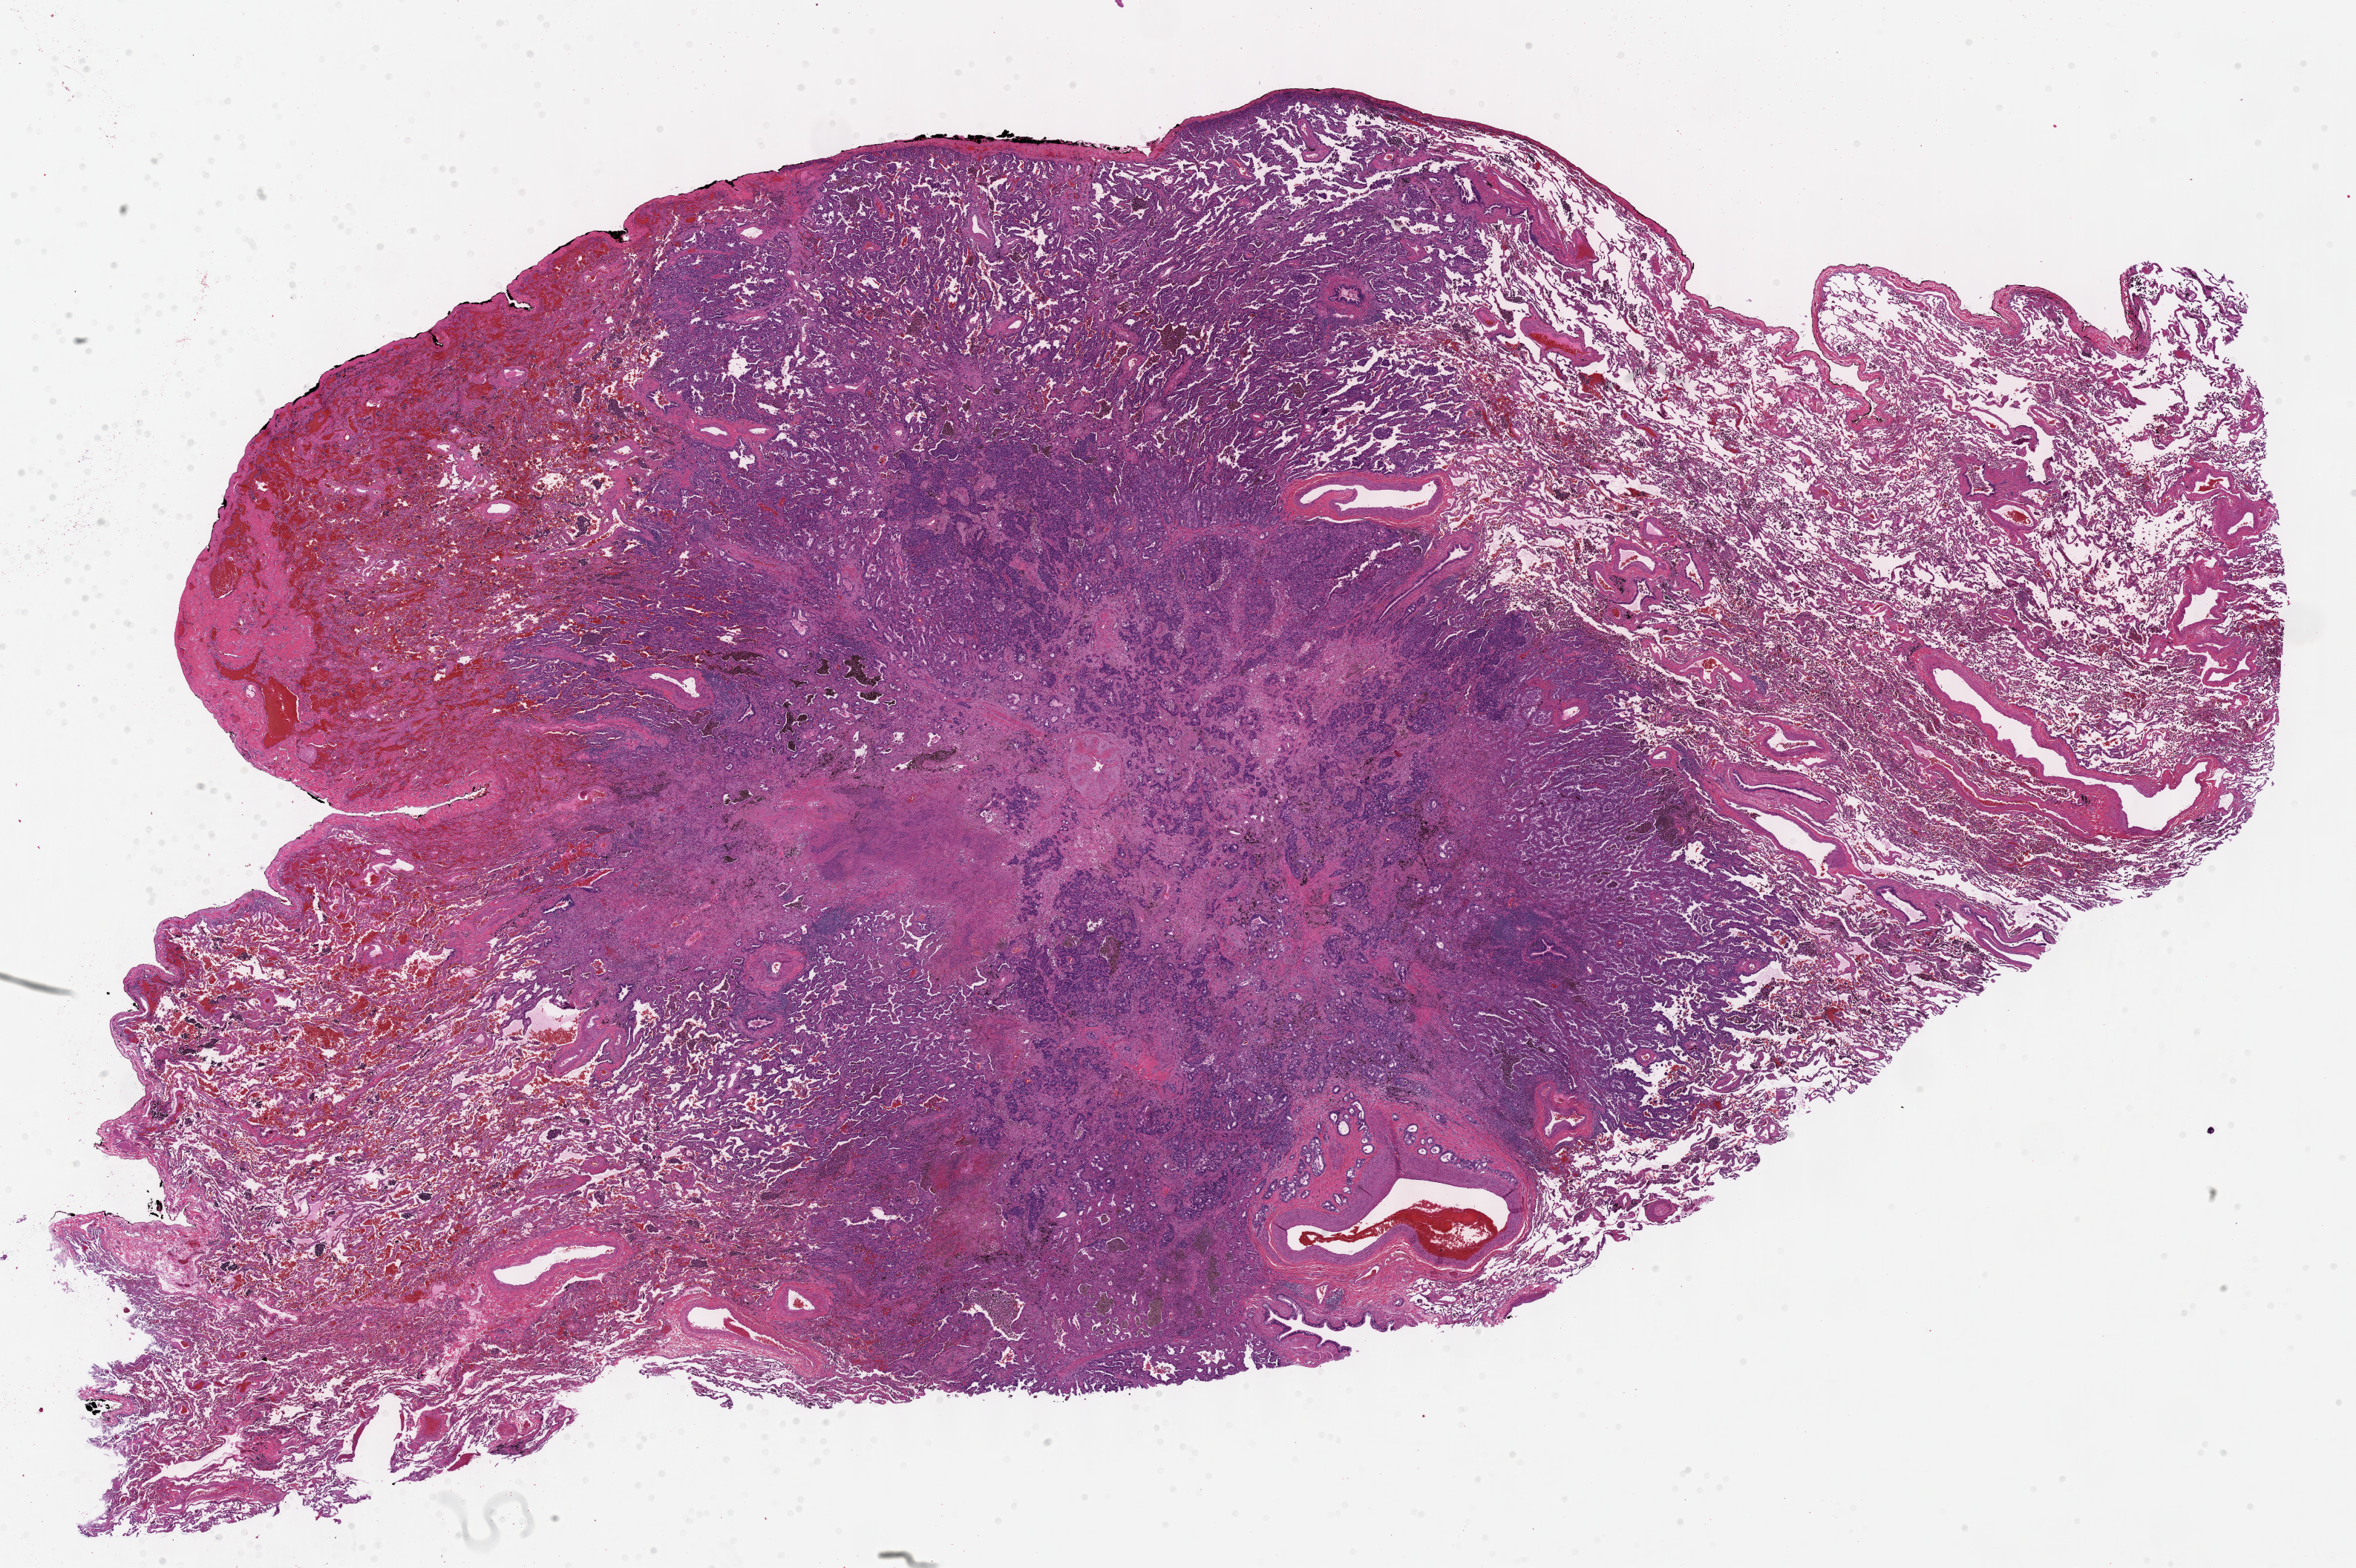
Hematoxylin and eosin (H&E) stained whole-slide image — low-resolution overview of the scanned area, about 25.7 x 17.1 mm (from a 40x scan). Formalin-fixed paraffin-embedded (FFPE) diagnostic section. Sample: primary tumour, lung. Patient: male, age at initial diagnosis 57 years.
Diagnosis: Adenocarcinoma, NOS (upper lobe, lung).